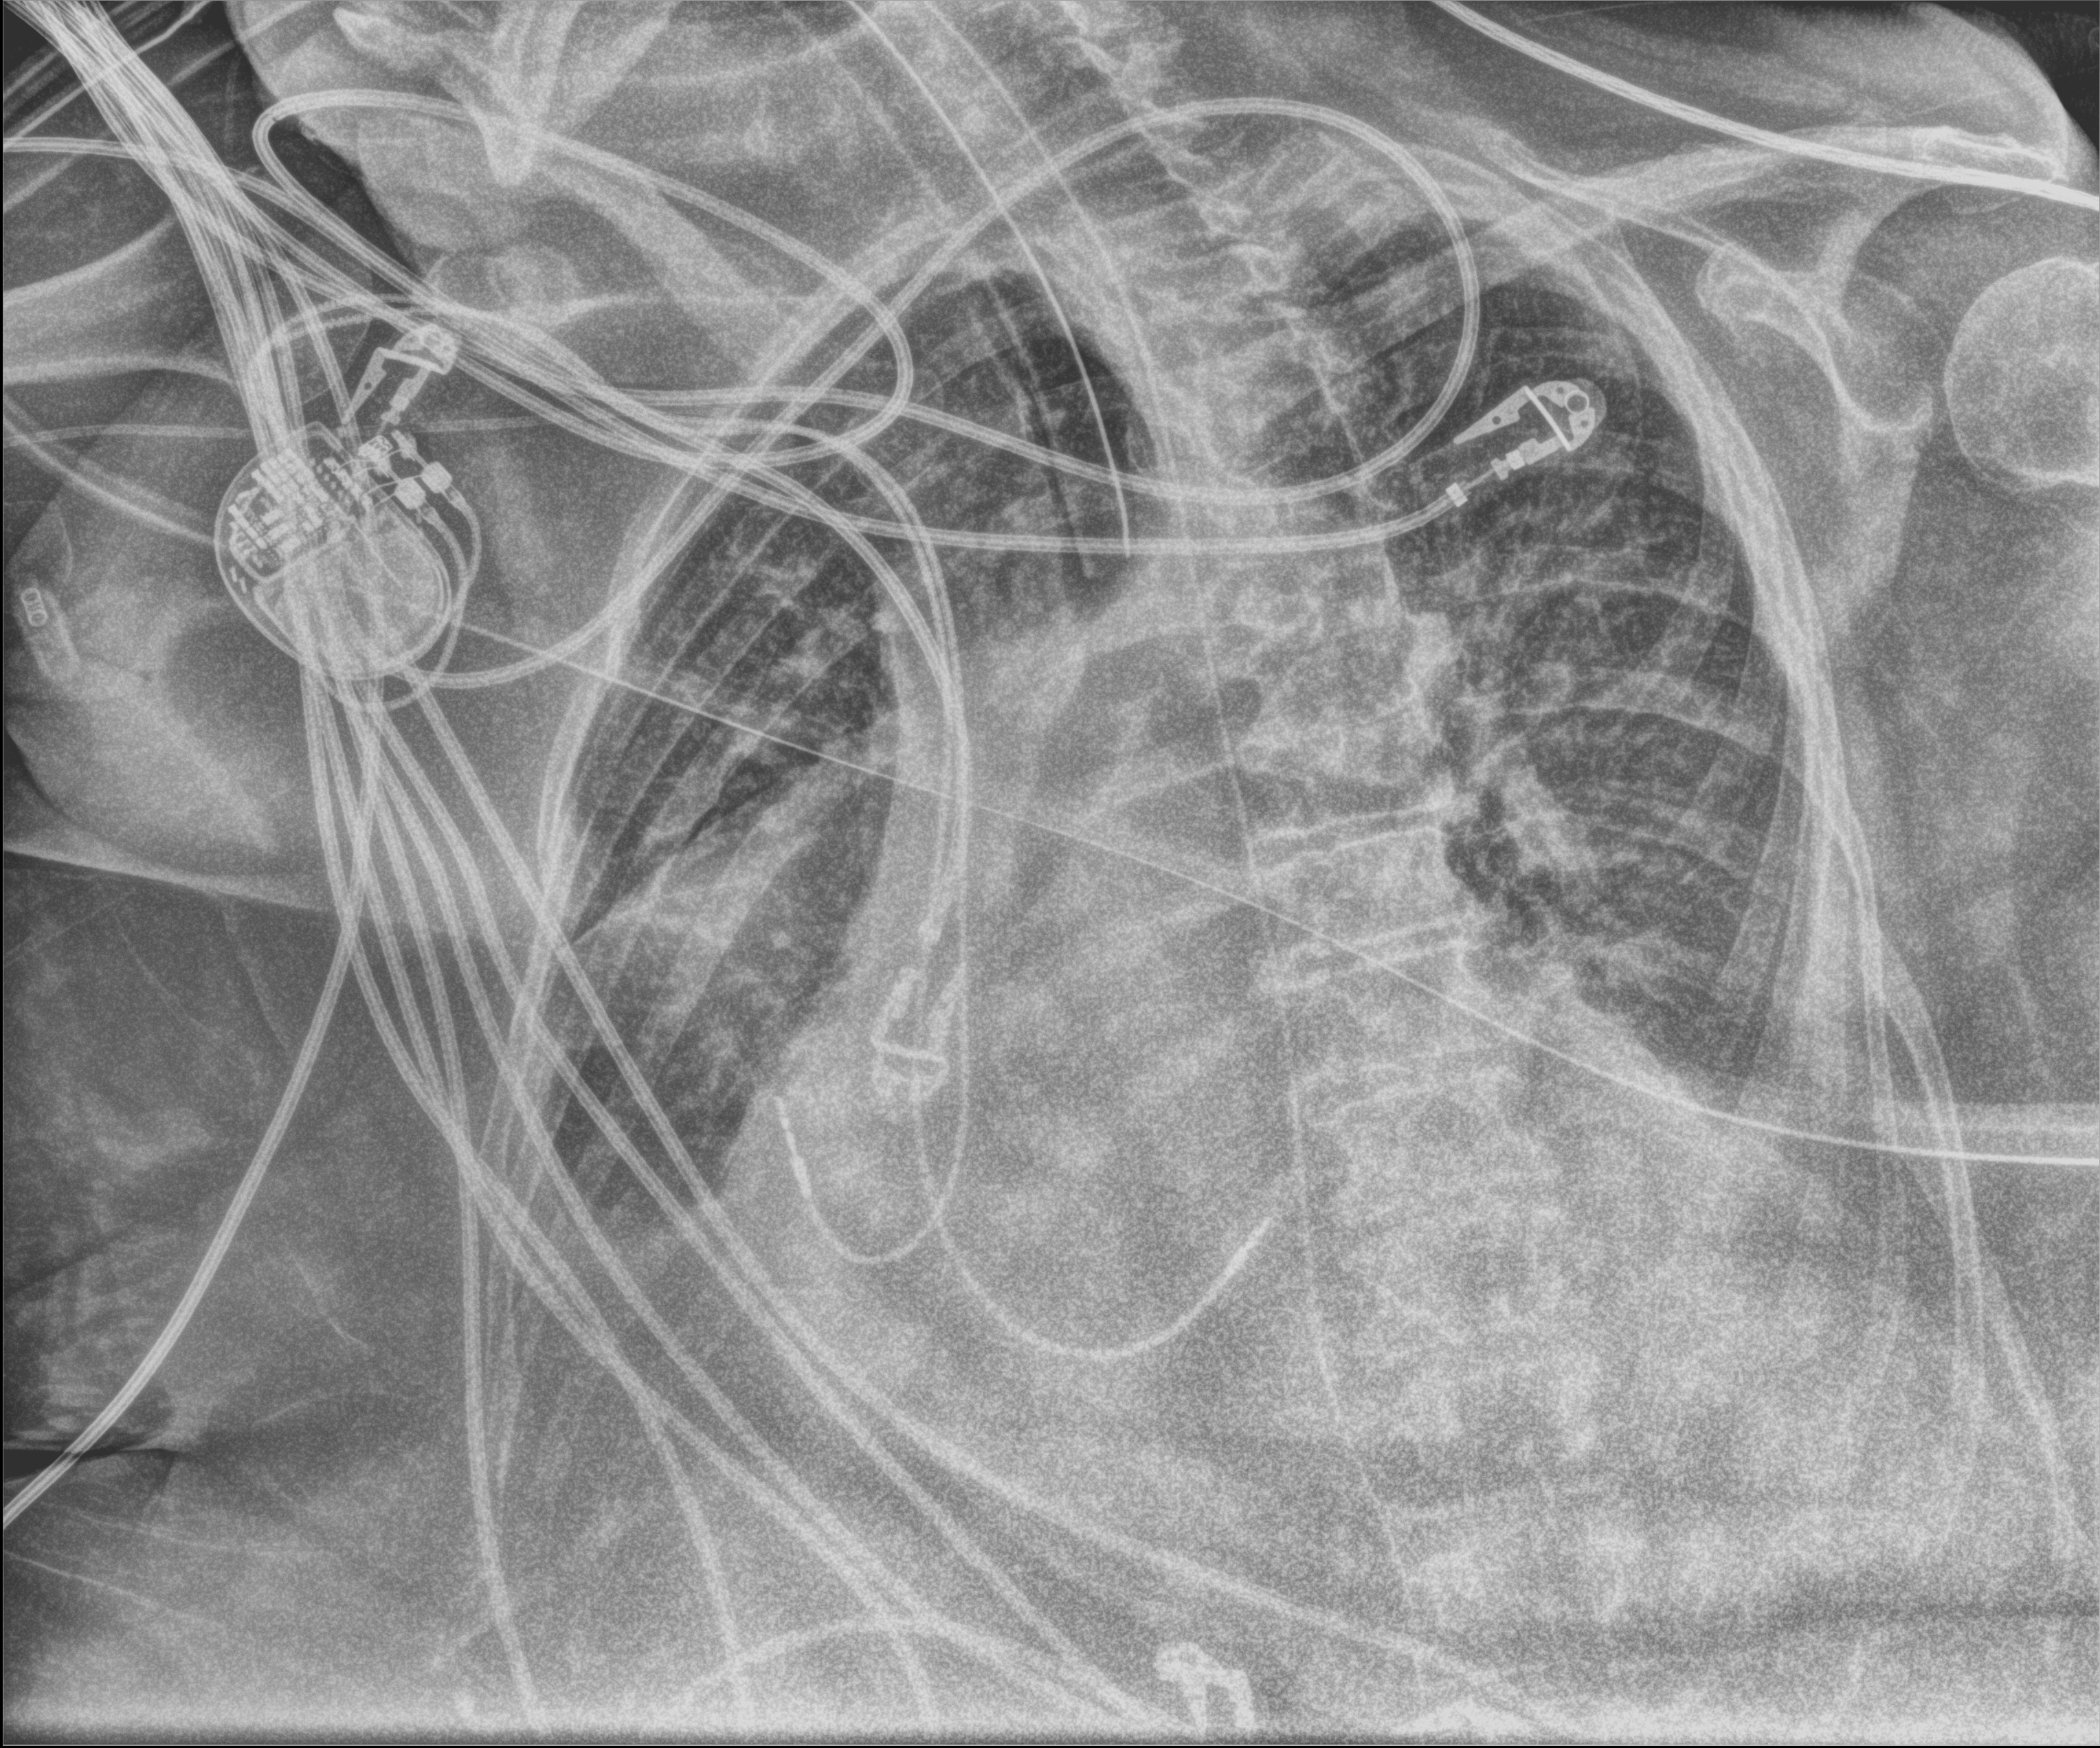
Chest X-ray (portable); anteroposterior (AP) projection. Patient hospitalised with COVID-19; female, aged 75–90 years.
Admission-level facts for this patient (not findings on this image; timing relative to this image not recorded):
- COPD (admission record): yes
- mechanically ventilated during this hospital stay: yes